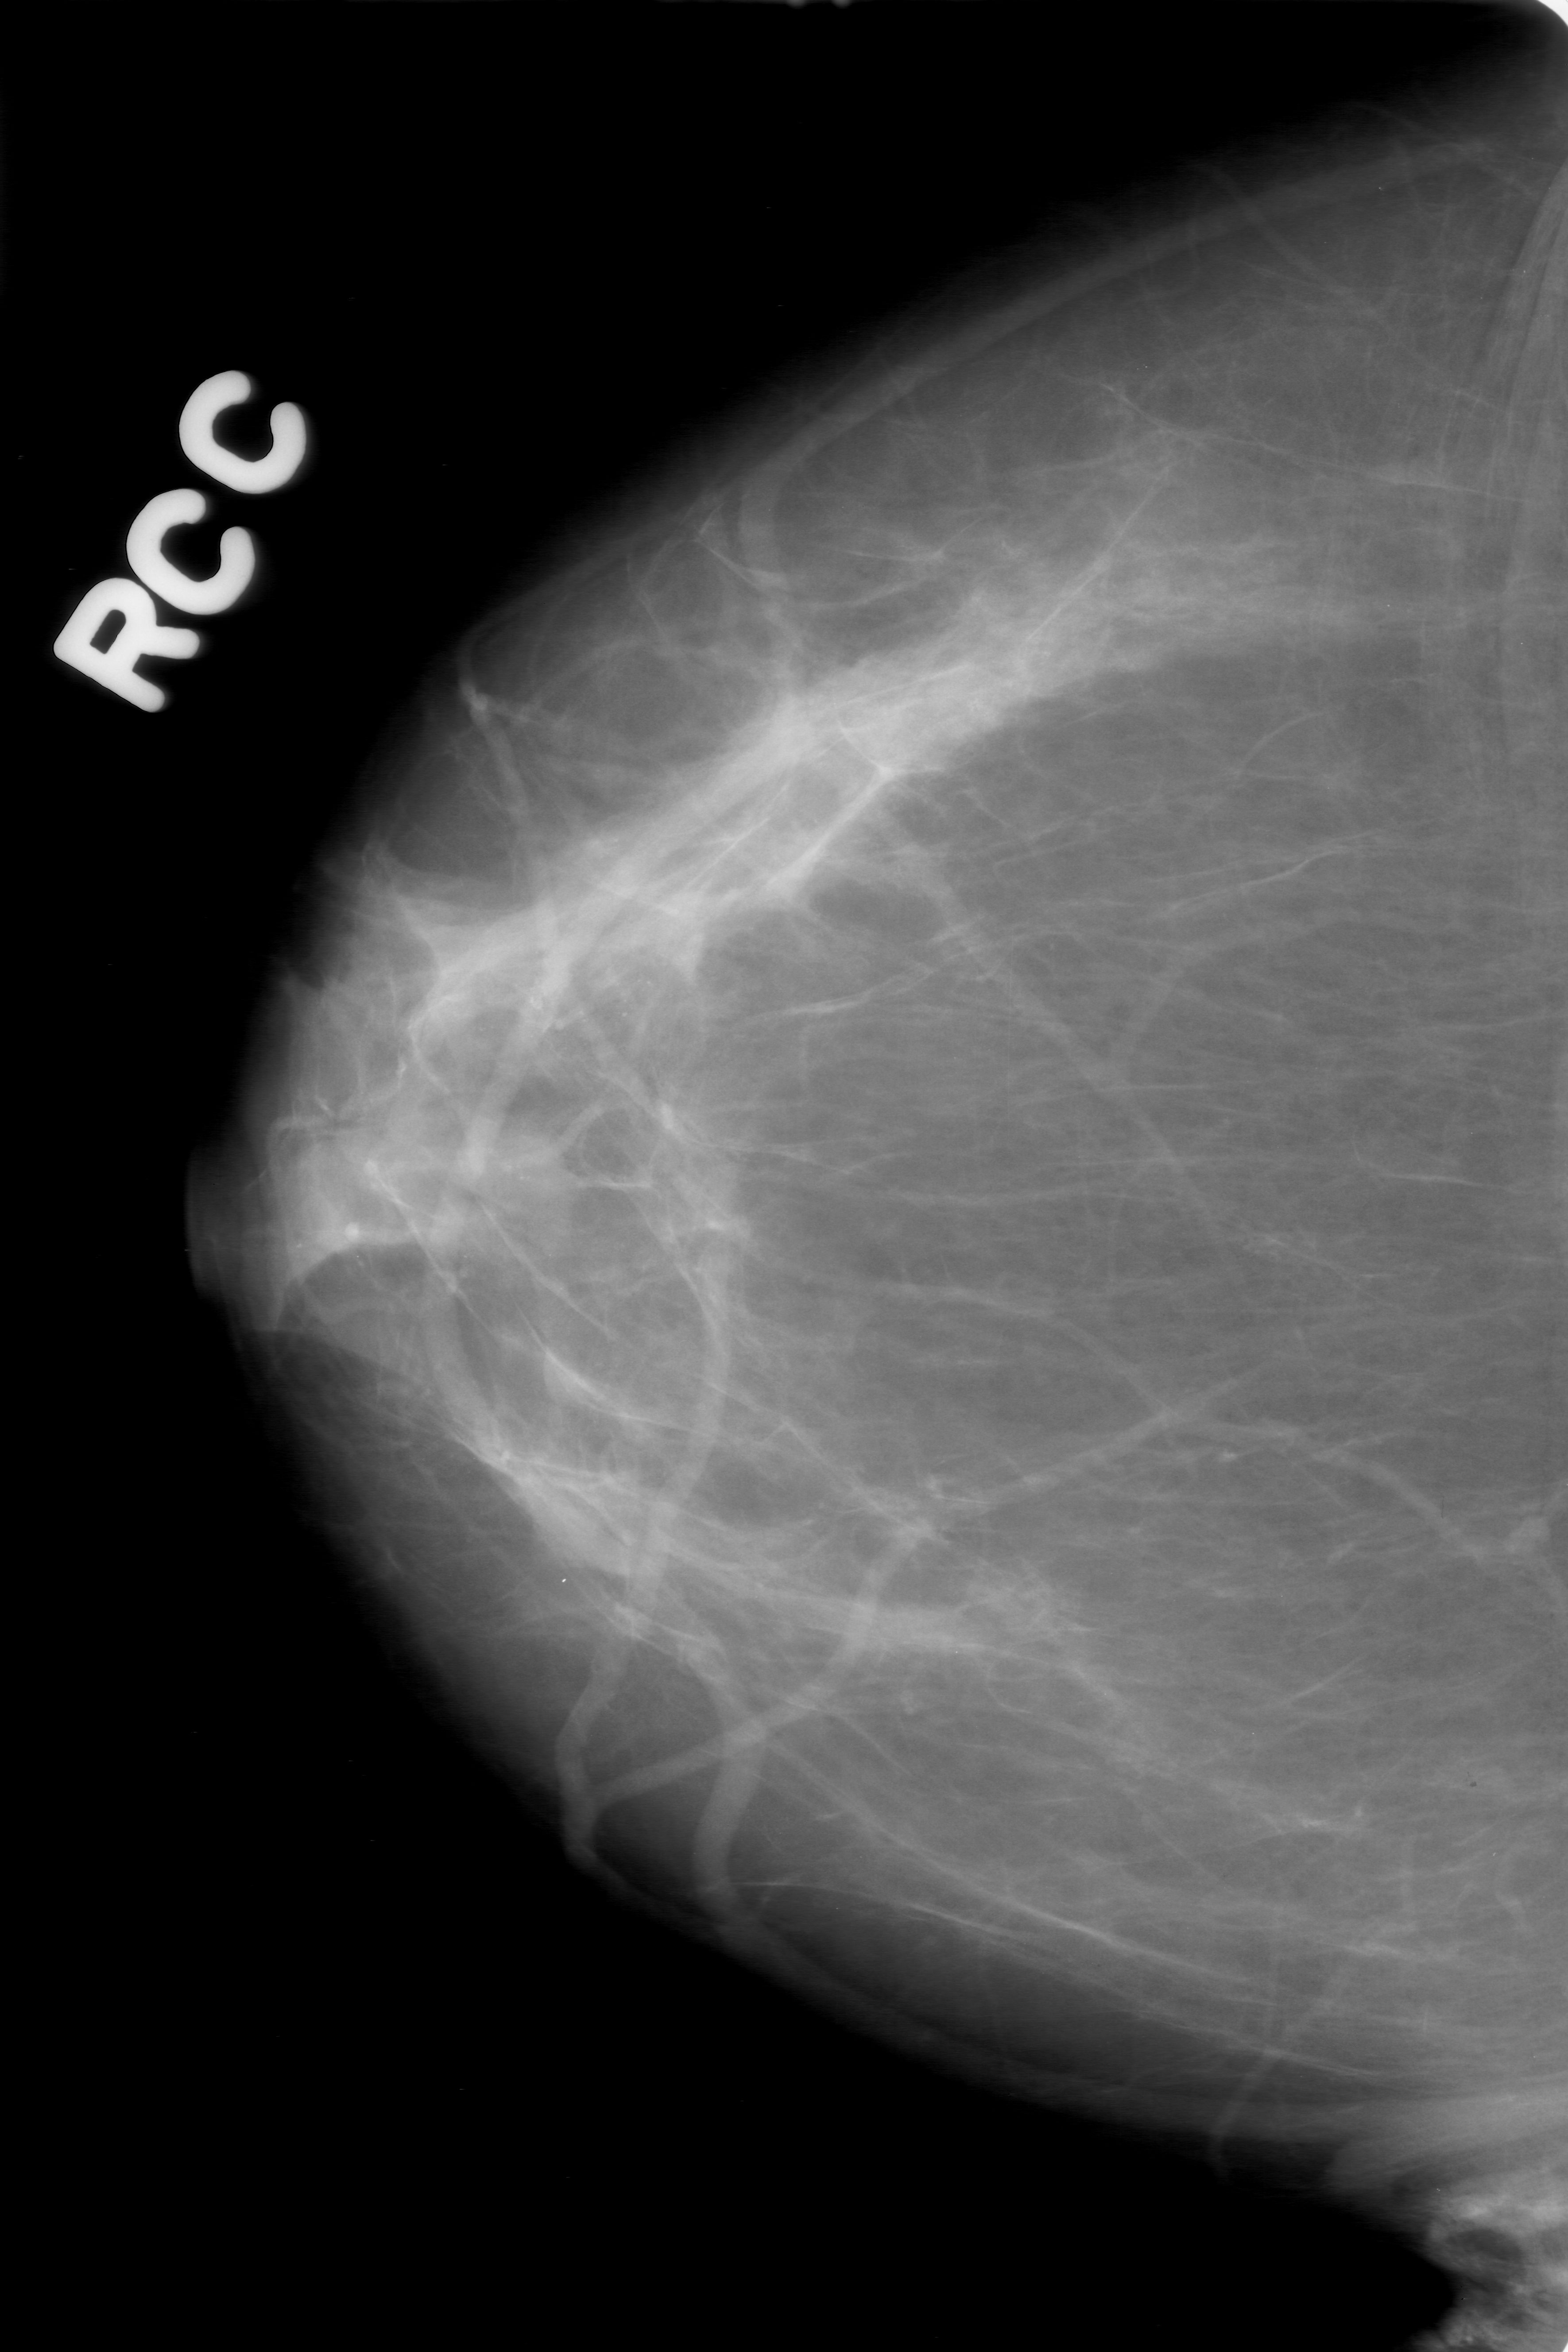
Scanned film-screen mammogram; right breast; craniocaudal (CC) view; BI-RADS breast density category 2 (scale 1–4); 1568 × 2352 image matrix.
Expert-marked regions of interest on this image (one box per marked abnormality):
- calcifications, morphology amorphous, distribution segmental; BI-RADS assessment category 0 (incomplete: needs additional imaging); pathology result (as recorded, not read from the image): malignant: box from (x=244, y=571) to (x=1087, y=1336) px